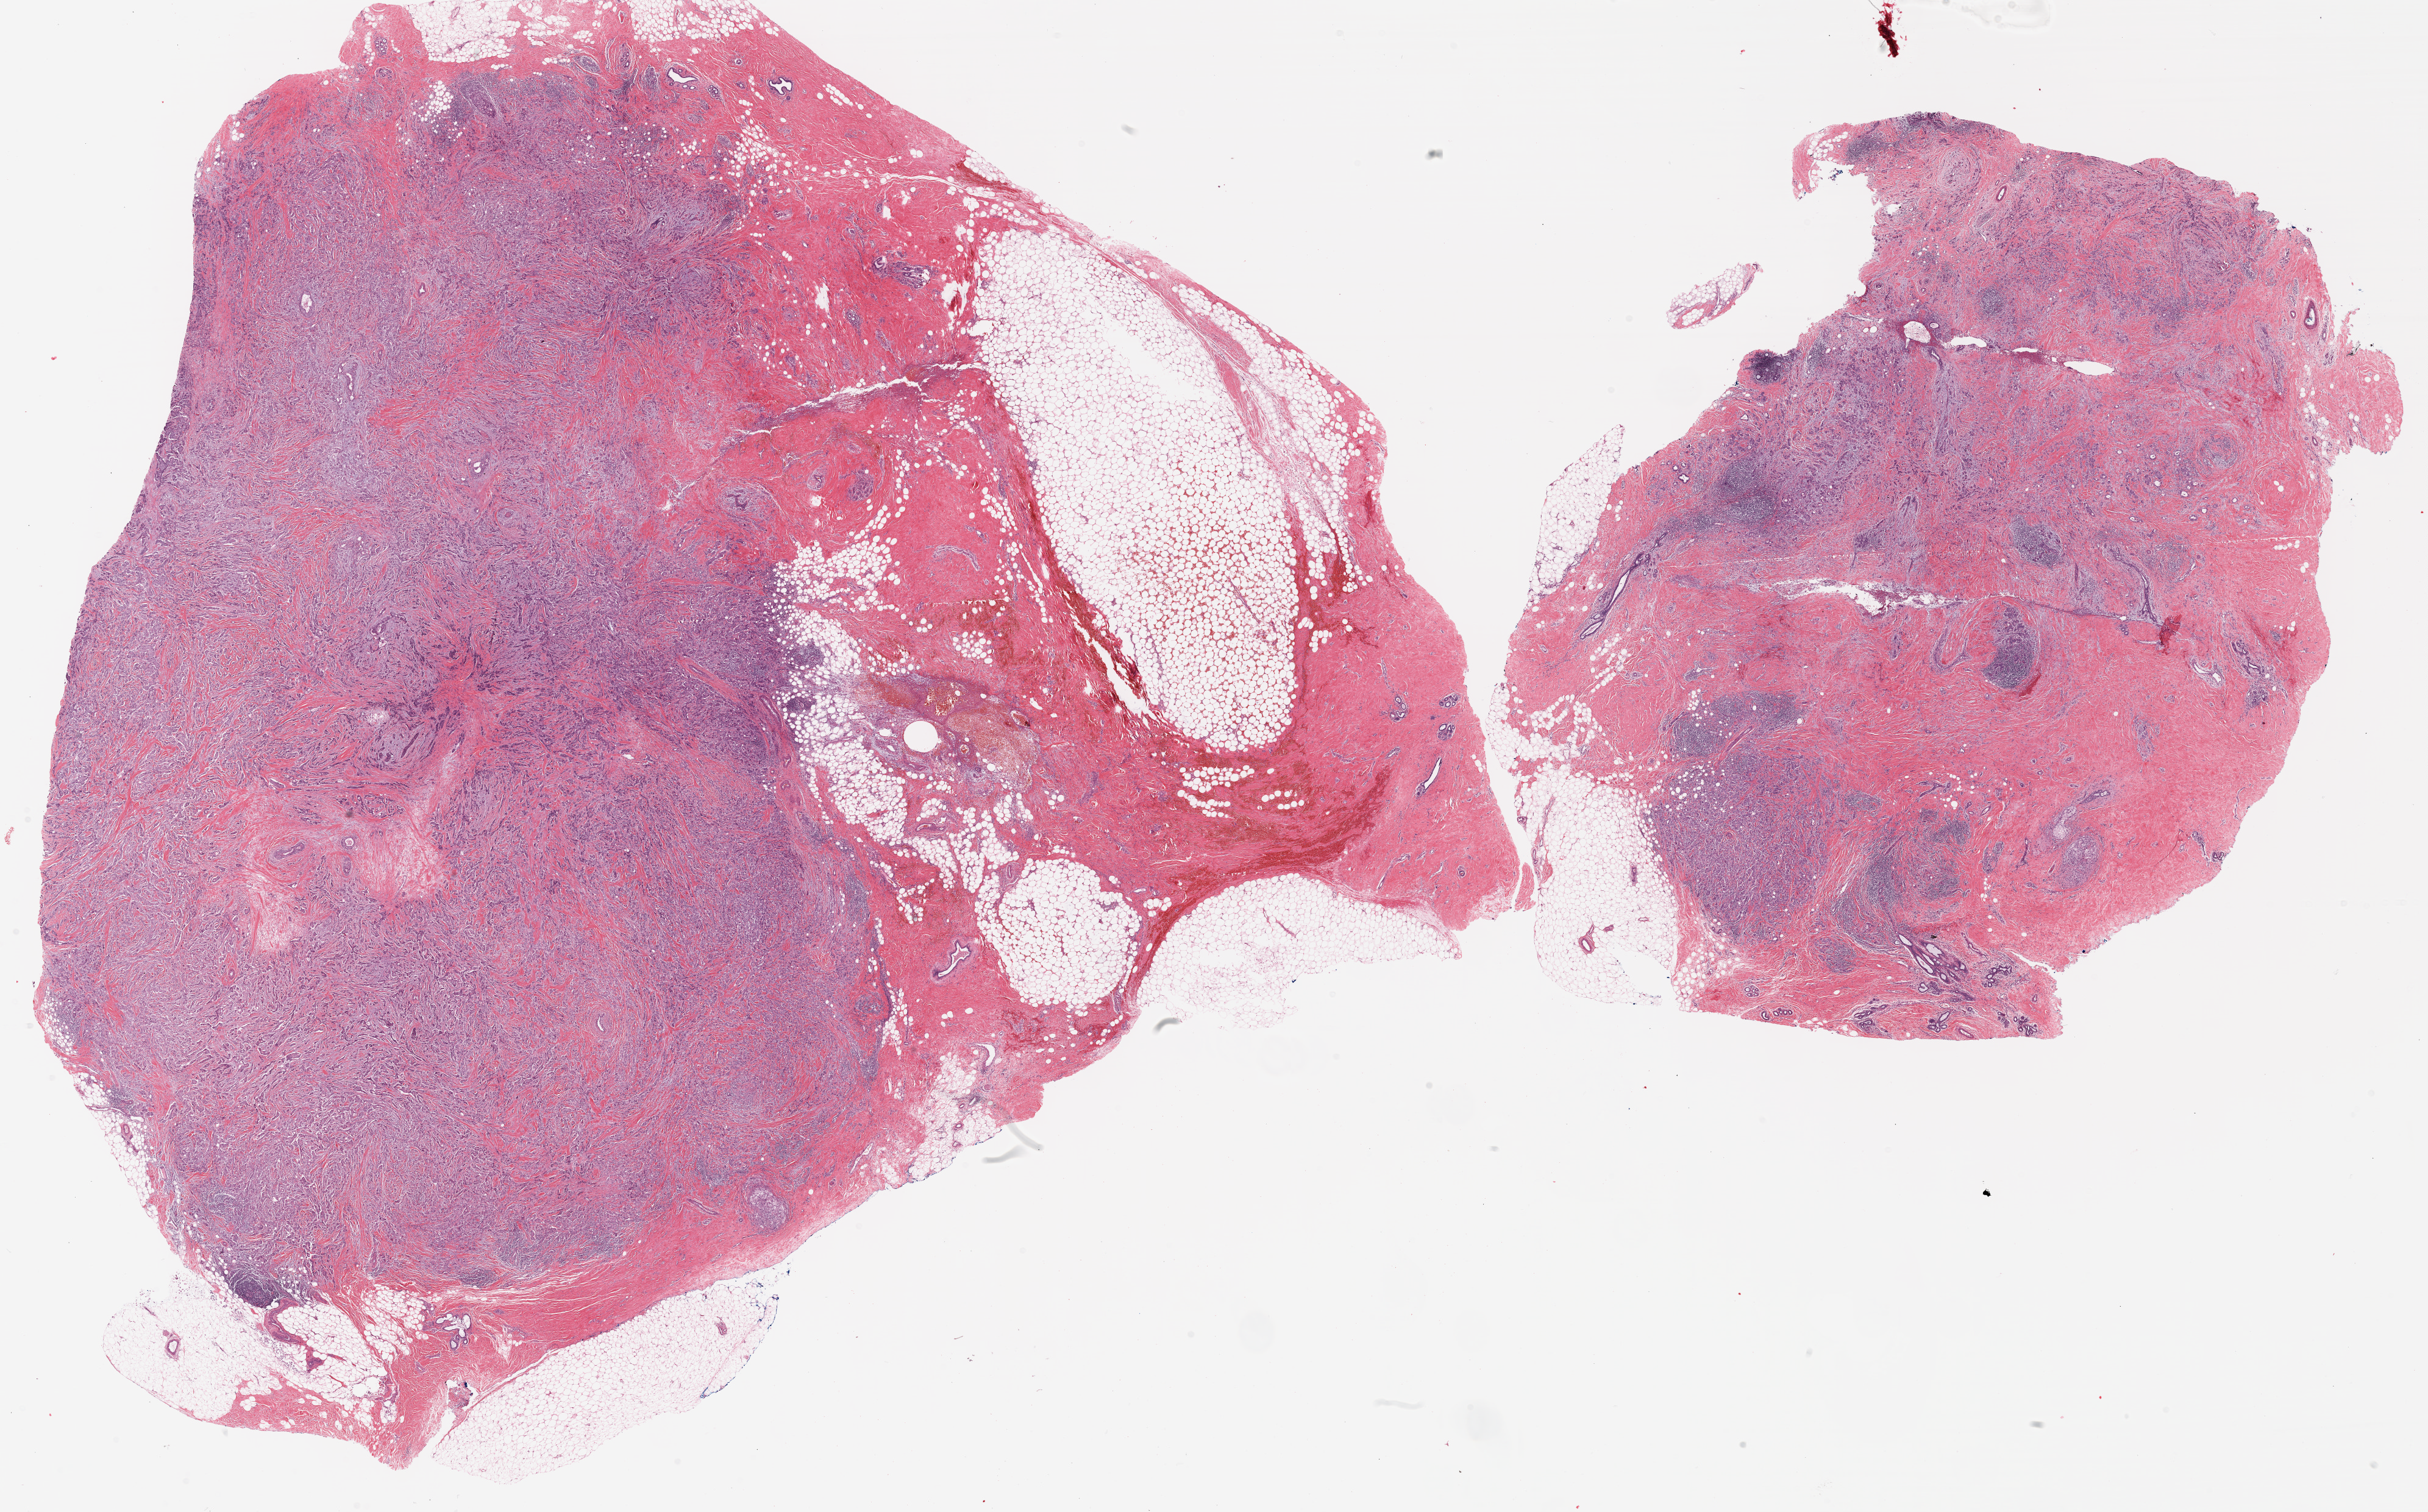
Digitized H&E tissue section (whole slide) — whole scanned area (about 31.8 x 19.8 mm) shown as a low-resolution overview. FFPE section. Sample: primary tumour, breast. Female, age 59 years at initial diagnosis.
- laterality: left
- pathologic diagnosis: Infiltrating duct carcinoma, NOS
- AJCC pathologic stage: IIB (6th edition)
- lymph nodes positive (case pathology): 2 of 19 examined